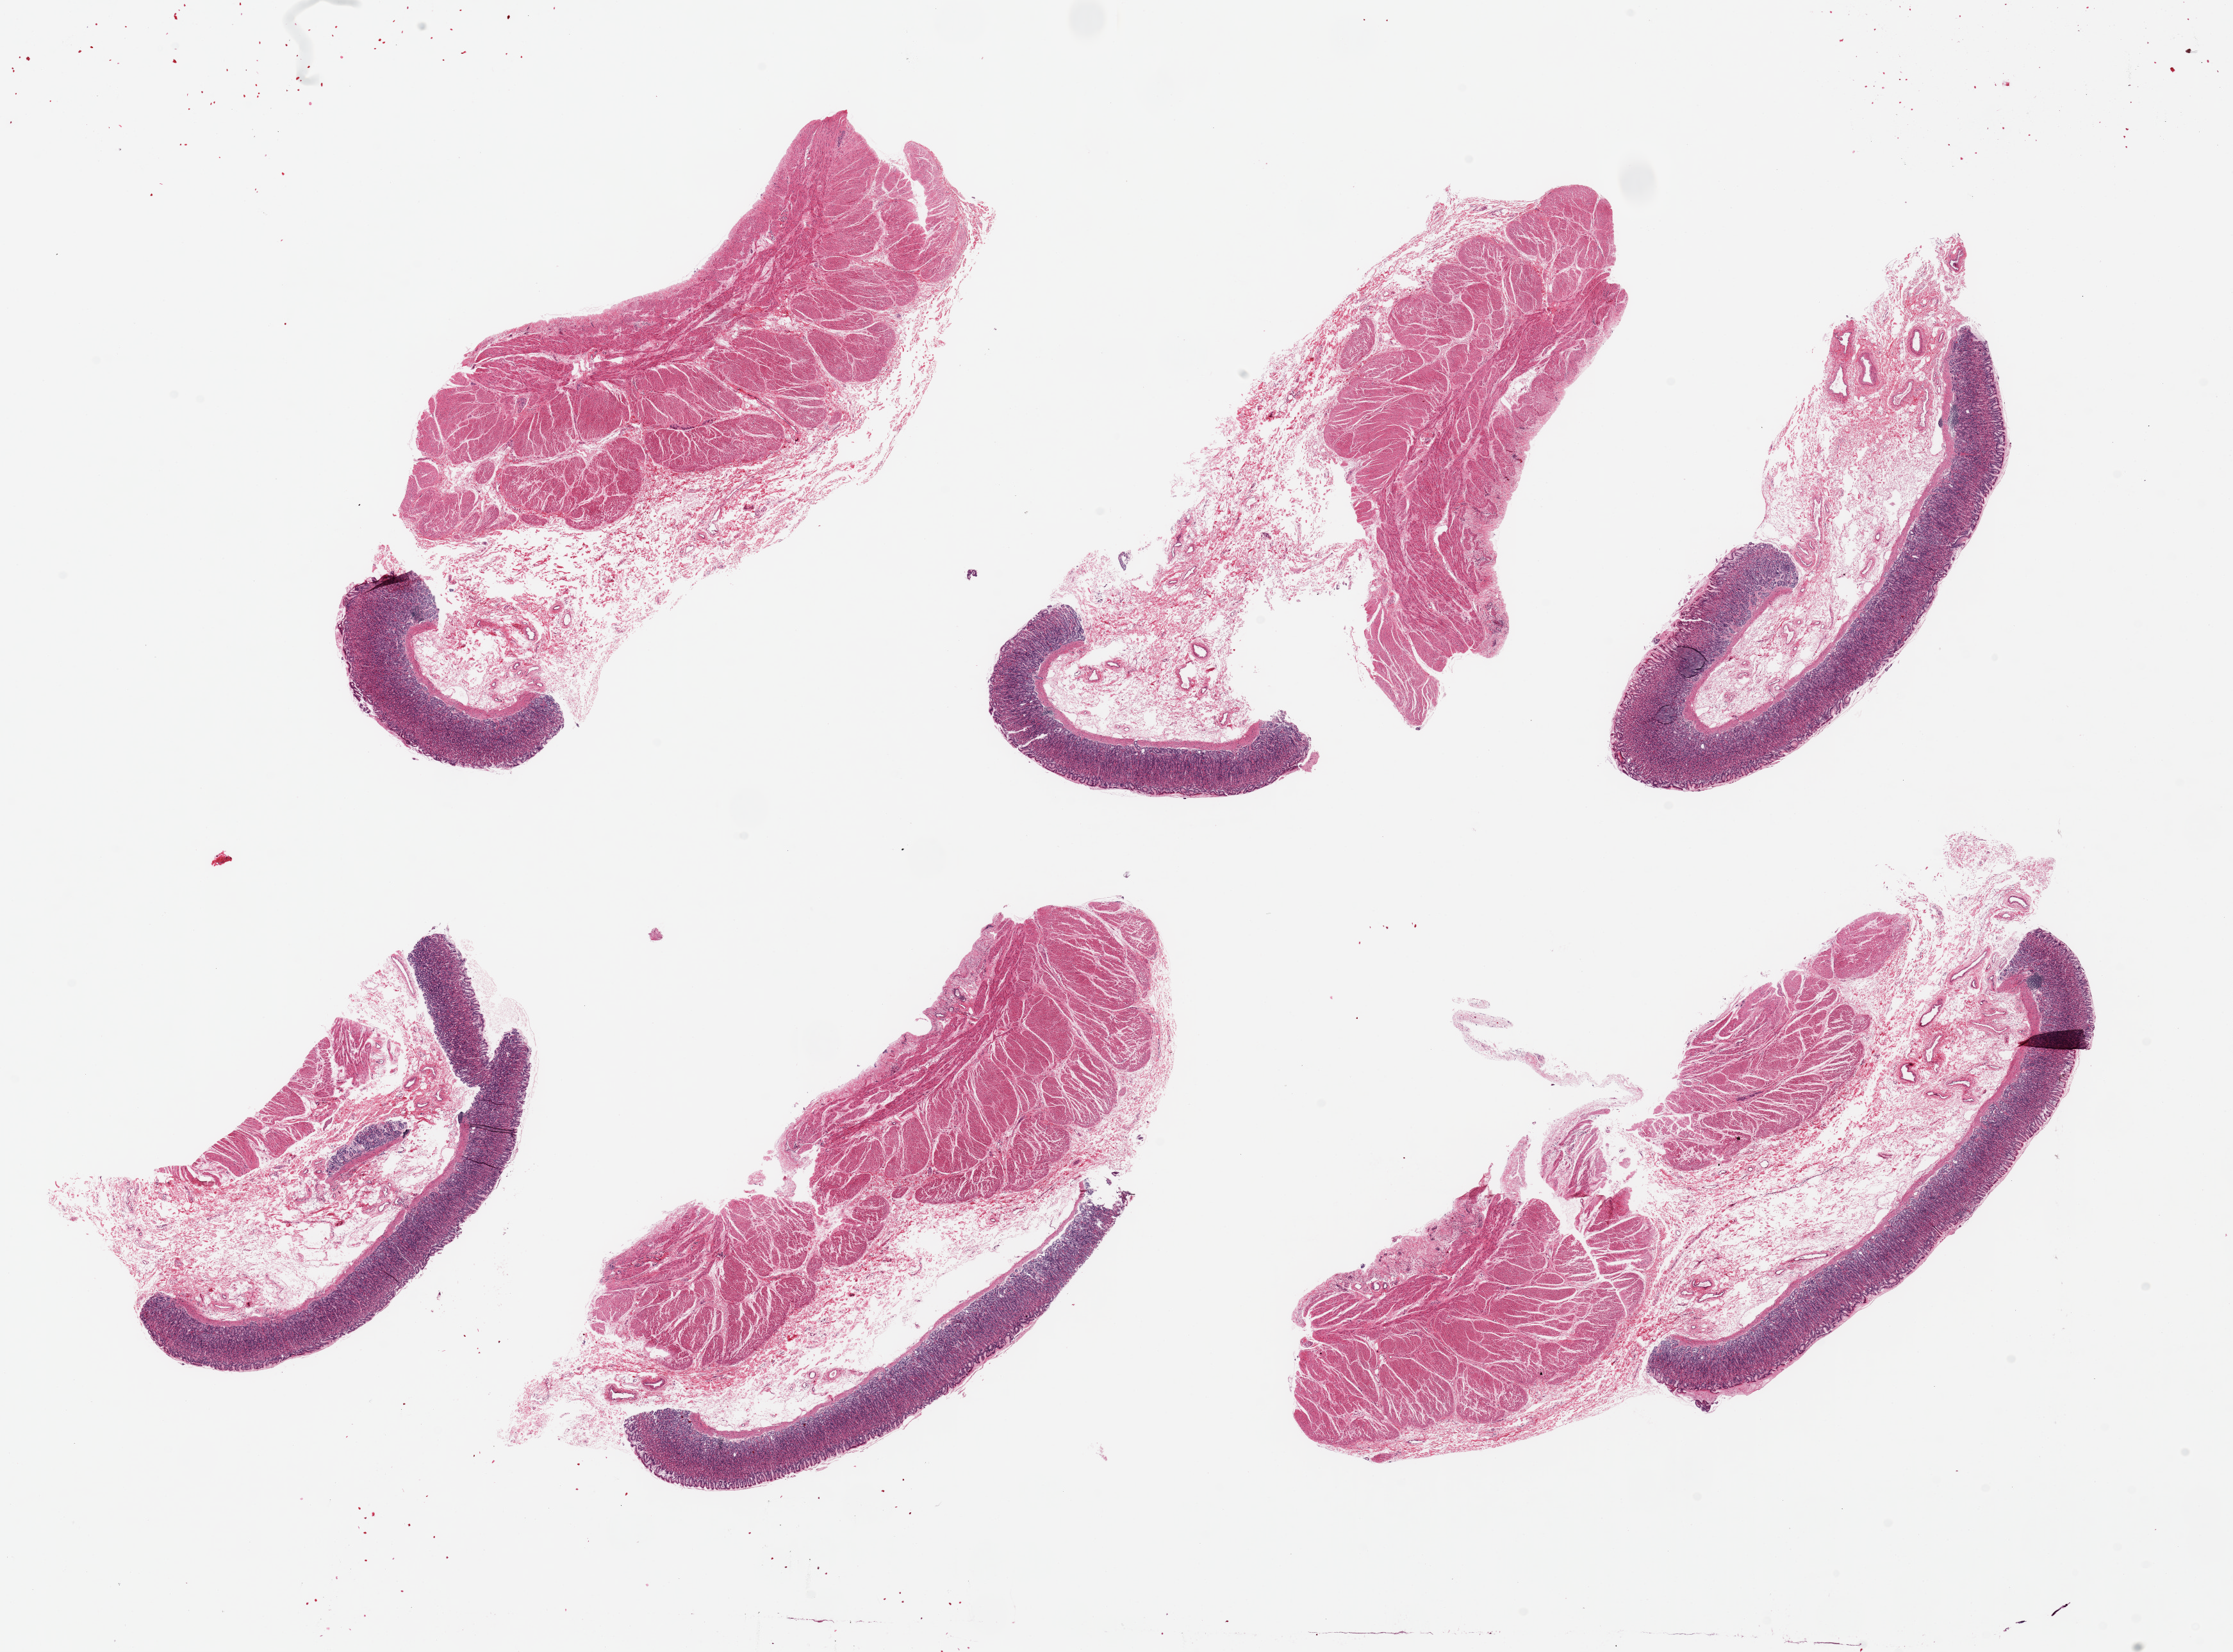
Whole-slide image, haematoxylin and eosin stain, brightfield, a low-resolution overview of the entire scanned area, about 27.6 x 20.4 mm (acquisition: 20x scan). PAXgene-fixed paraffin-embedded (PFPE) section. Target tissue: stomach. Tissue donor sample. Female donor.
- reviewer comment on this tissue sample: 6 pieces, up to 12x6mm; good oxyntic mucosa; well preserved